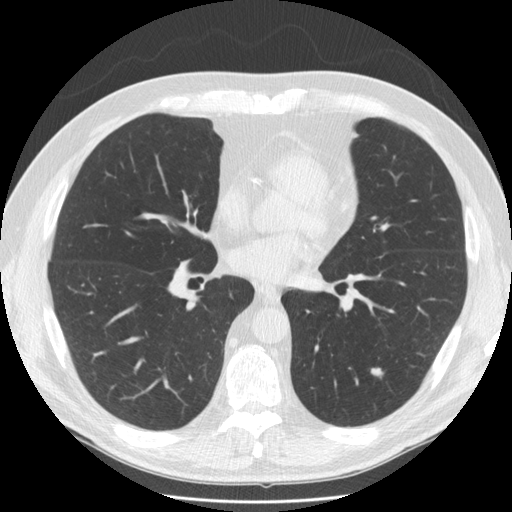
Axial slice from a low-dose chest CT screening exam, third annual screen, lung window (W 1500 / L -600 HU), standard (soft-tissue) reconstruction kernel (STANDARD). Male participant, aged 58 years at enrolment. Former smoker at enrolment.
Expert-annotated lung lesion, bounding box [x1, y1, x2, y2] px = [358, 358, 397, 389]. Screening reader's record for this exam (one nodule recorded; not confirmed to be the boxed lesion): non-calcified nodule or mass ≥4 mm, left lower lobe, 10 × 7 mm, smooth margins, soft tissue attenuation, pre-existing on the prior screen: yes; interval growth: yes.